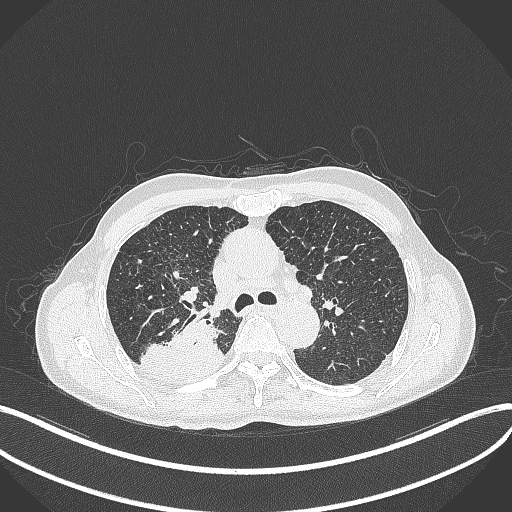
Chest CT, one axial slice; slice 303 of 428 in the series (ordered by position); reconstruction kernel B70f; lung window (W 1500 / L -600 HU); 1 mm slice thickness; 512 × 512 image matrix, field of view 400 × 400 mm. Patient: male, 79 years. From the clinical record (not read from this slice): clinical TNM (as recorded): T3 N0 M0.
Outlined on this slice (rectangle marked by the reading radiologist):
- lung tumour (recorded histology: adenocarcinoma): bounding box [x1, y1, x2, y2] px = [139, 312, 227, 379]